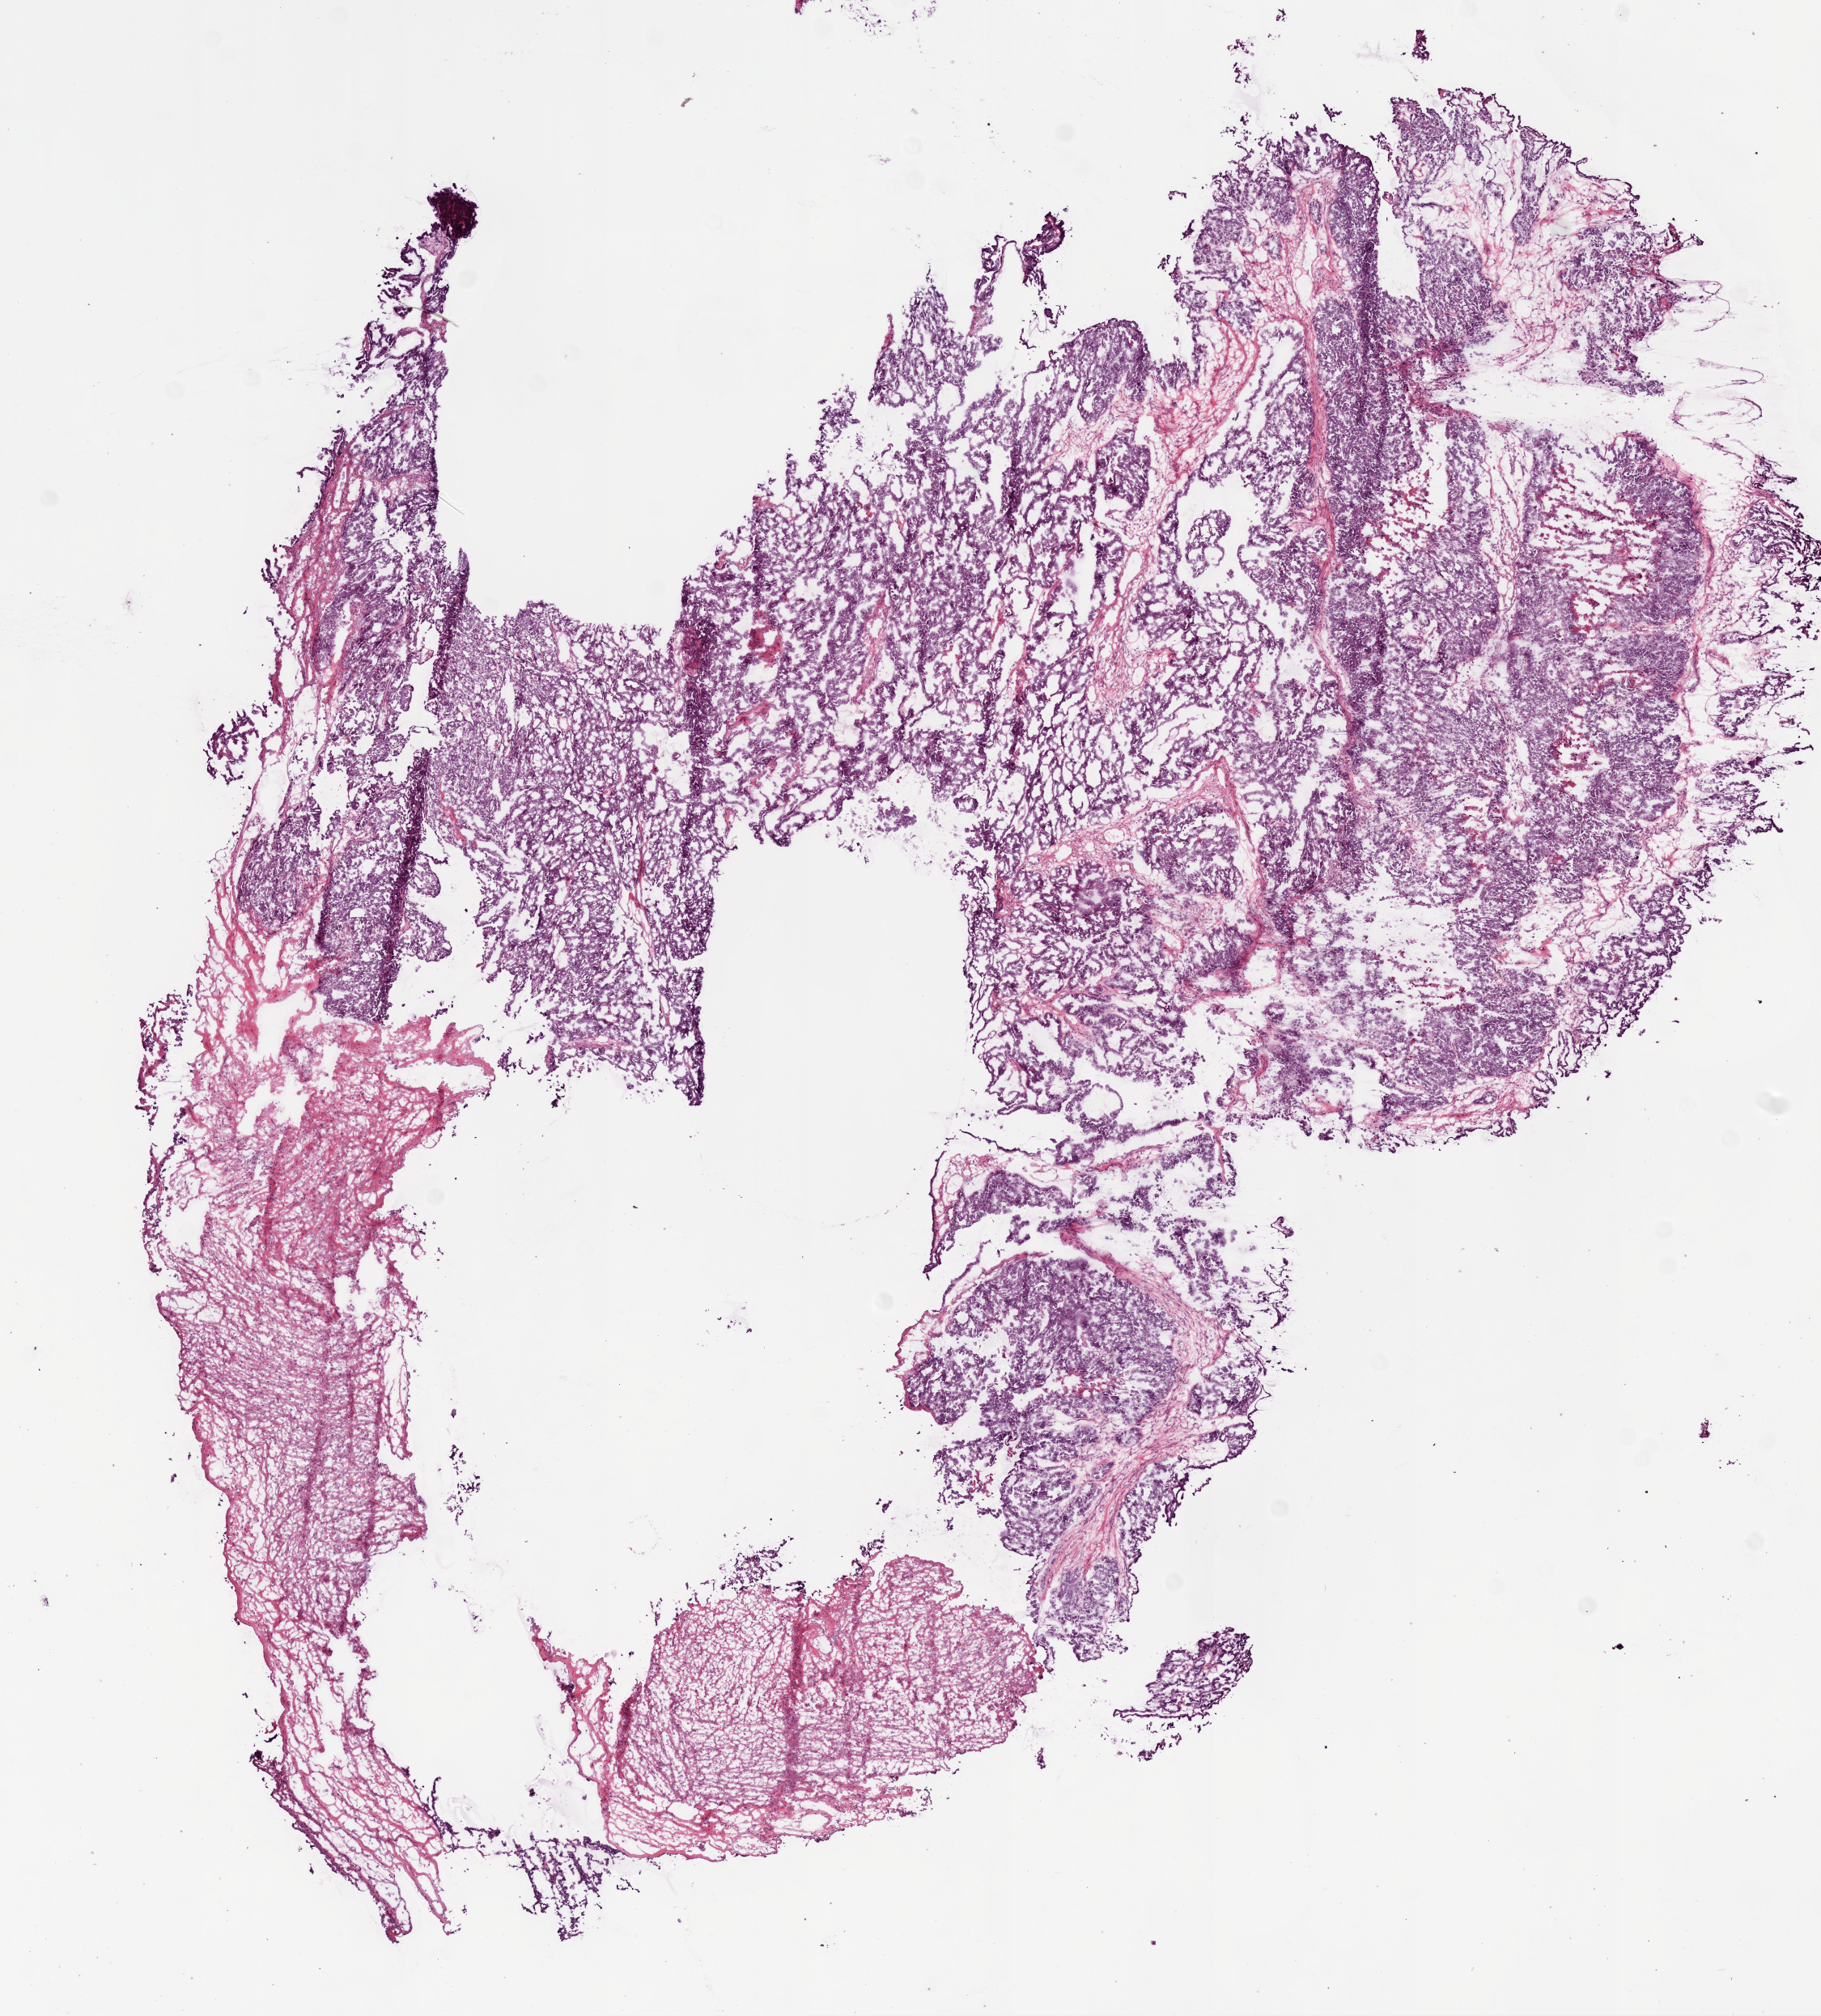
Digitized H&E tissue section (whole slide) — whole scanned area (about 9.0 x 10.0 mm, from a 20x scan) shown as a low-resolution overview, frozen section from the bottom of the tissue portion, ovary, primary tumour sample. Patient: female, age at initial diagnosis 68 years. Histologic grade: G3 (poorly differentiated). Composition of this section per pathologist review: tumour cells 75%, tumour nuclei 85%, normal cells 0%, stromal cells 23%, necrosis 2%.
* FIGO stage: IV
* histologic diagnosis: Serous cystadenocarcinoma, NOS
* laterality: bilateral